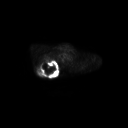
FDG PET of an extremity soft-tissue mass (from a PET/CT study), one axial slice. Position 212 of 267 along the scan axis. 3.27 mm slice thickness. 128 × 128 image matrix, field of view 700 × 700 mm. Male patient, age 61 years. From the clinical record (not read from this slice): histological type: pleiomorphic spindle cell undifferentiated; grade: high; site of the primary tumour: right parascapusular.
Outlined on this slice (expert contour drawn on MRI and transferred to this co-registered scan by the dataset authors):
- gross tumour volume including surrounding oedema: box from (x=36, y=59) to (x=60, y=76) px
- gross tumour volume (mass): (x=41, y=60)–(x=57, y=75)